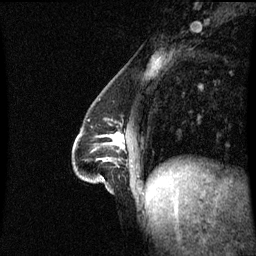
Breast MRI (dynamic contrast-enhanced), one sagittal slice. Dynamic contrast-enhanced series, image 2 of 3 at this slice position (ordered by acquisition). 1.5 T. TE 4.2 ms, TR 8.9 ms. 2.2 mm slice thickness. 256 × 256 image matrix, field of view 210 × 210 mm. Female patient, age 47 years. From the clinical record (not read from this slice): setting: breast cancer imaged before/during neoadjuvant chemotherapy; receptor status: HR-positive, HER2-negative.
Structures marked on this image (semi-automatic segmentation, software-assisted and operator-edited):
- analysis volume of interest (the breast-tissue region the enhancement analysis was run in; not a lesion): box from (x=74, y=131) to (x=125, y=193) px
- tumour enhancement mask (voxels above the 70 % enhancement threshold inside the analysis volume of interest): (x=114, y=136)–(x=121, y=145)